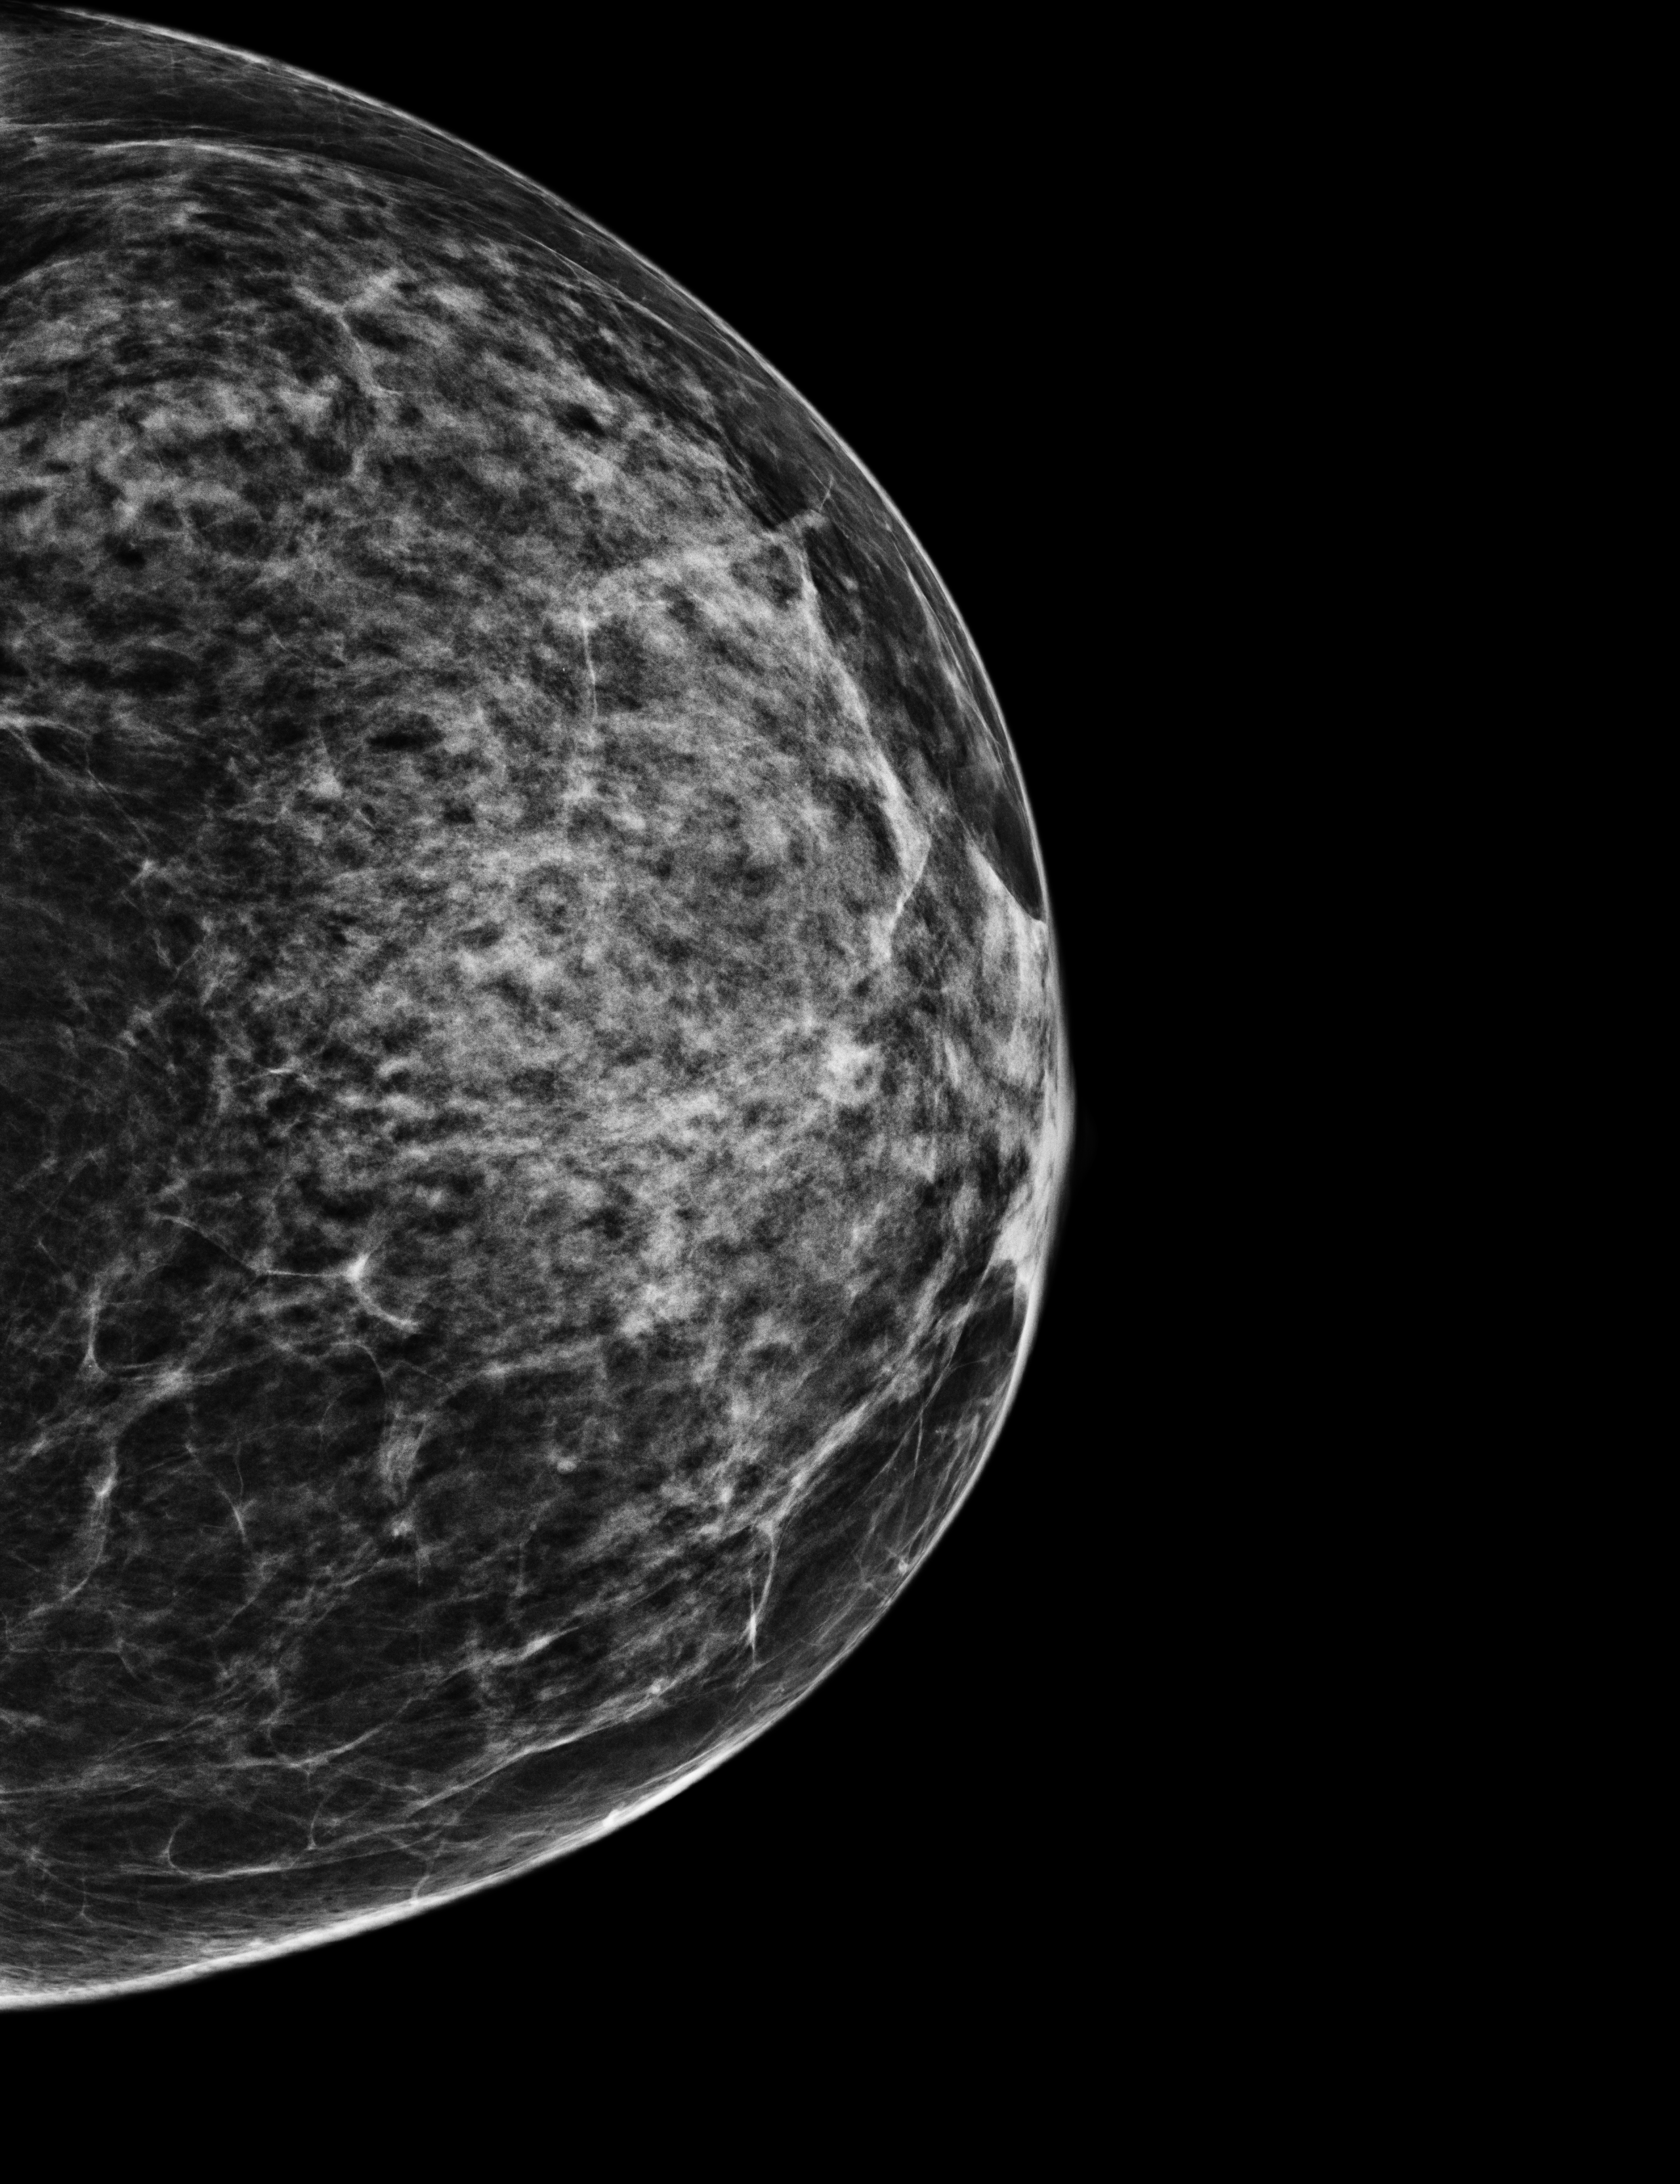
Annual screening mammography examination; compressed breast thickness 48 mm. Female patient, age 59 years.
Image type: full-field digital mammogram. Breast: left. Projection: cranio-caudal projection.